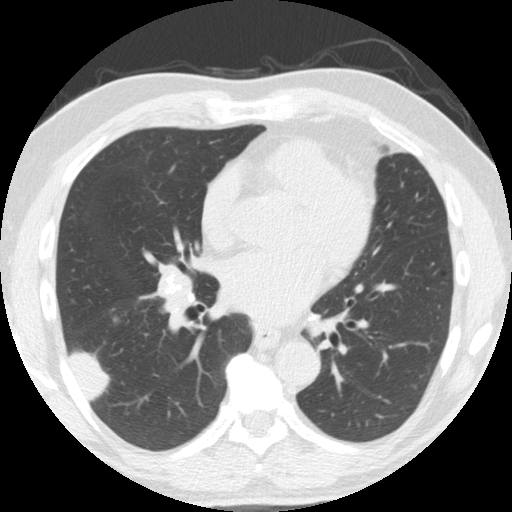
Low-dose screening chest CT, one axial slice; slice 81 of 174 in the series (ordered by position); reconstruction kernel STANDARD; 120 kVp; lung window (W 1500 / L -600 HU); 2.5 mm slice thickness; 512 × 512 image matrix, field of view 341 × 341 mm.
Outlined on this slice (outlined manually by an expert reader):
- lesion 1 (tumor, lower lobe of right lung): bounding box <70,351,109,401> (left, top, right, bottom; pixels)